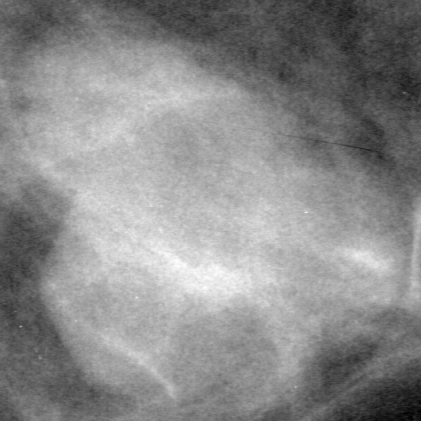
Crop from a digitized film mammogram around one marked abnormality; right breast; CC view; BI-RADS breast density category 3 (scale 1–4).
Mass, shape lobulated, margins circumscribed; BI-RADS assessment category 4; subtlety rating 5 on a 1 (subtle) to 5 (obvious) scale; pathology result (as recorded, not read from the image): benign.